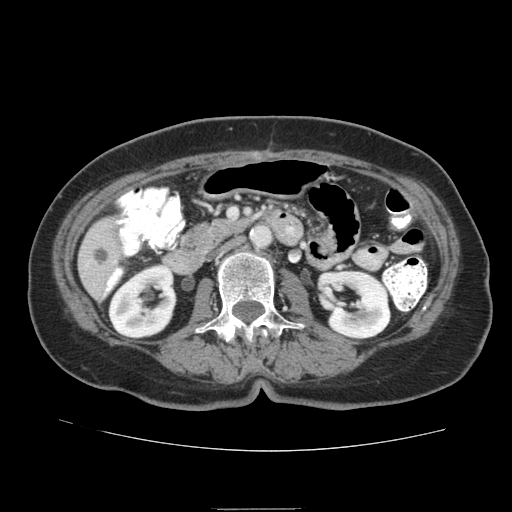
Contrast-enhanced abdominal CT (liver protocol), one axial slice; position 24 of 95 along the scan axis; reconstruction kernel STANDARD; soft-tissue window (W 400 / L 40 HU); 2.5 mm slice thickness; 512 × 512 image matrix, field of view 360 × 360 mm. Case-level facts recorded for this patient, not image findings: diagnosis: hepatocellular carcinoma (patient treated with transarterial chemoembolisation; whether this scan precedes or follows treatment is not stated here); TNM stage (as recorded): Stage-IVA; Child-Pugh class: B; tumour nodularity: uninodular.
Annotated regions visible in this slice (semi-automatic segmentation, software-assisted and operator-edited):
- liver parenchyma outside the tumour (the mass and vessels are separate outlines, so this box may not span the whole liver): bounding box [x1, y1, x2, y2] px = [78, 216, 122, 302]
- liver vessels: [105, 220, 122, 293]